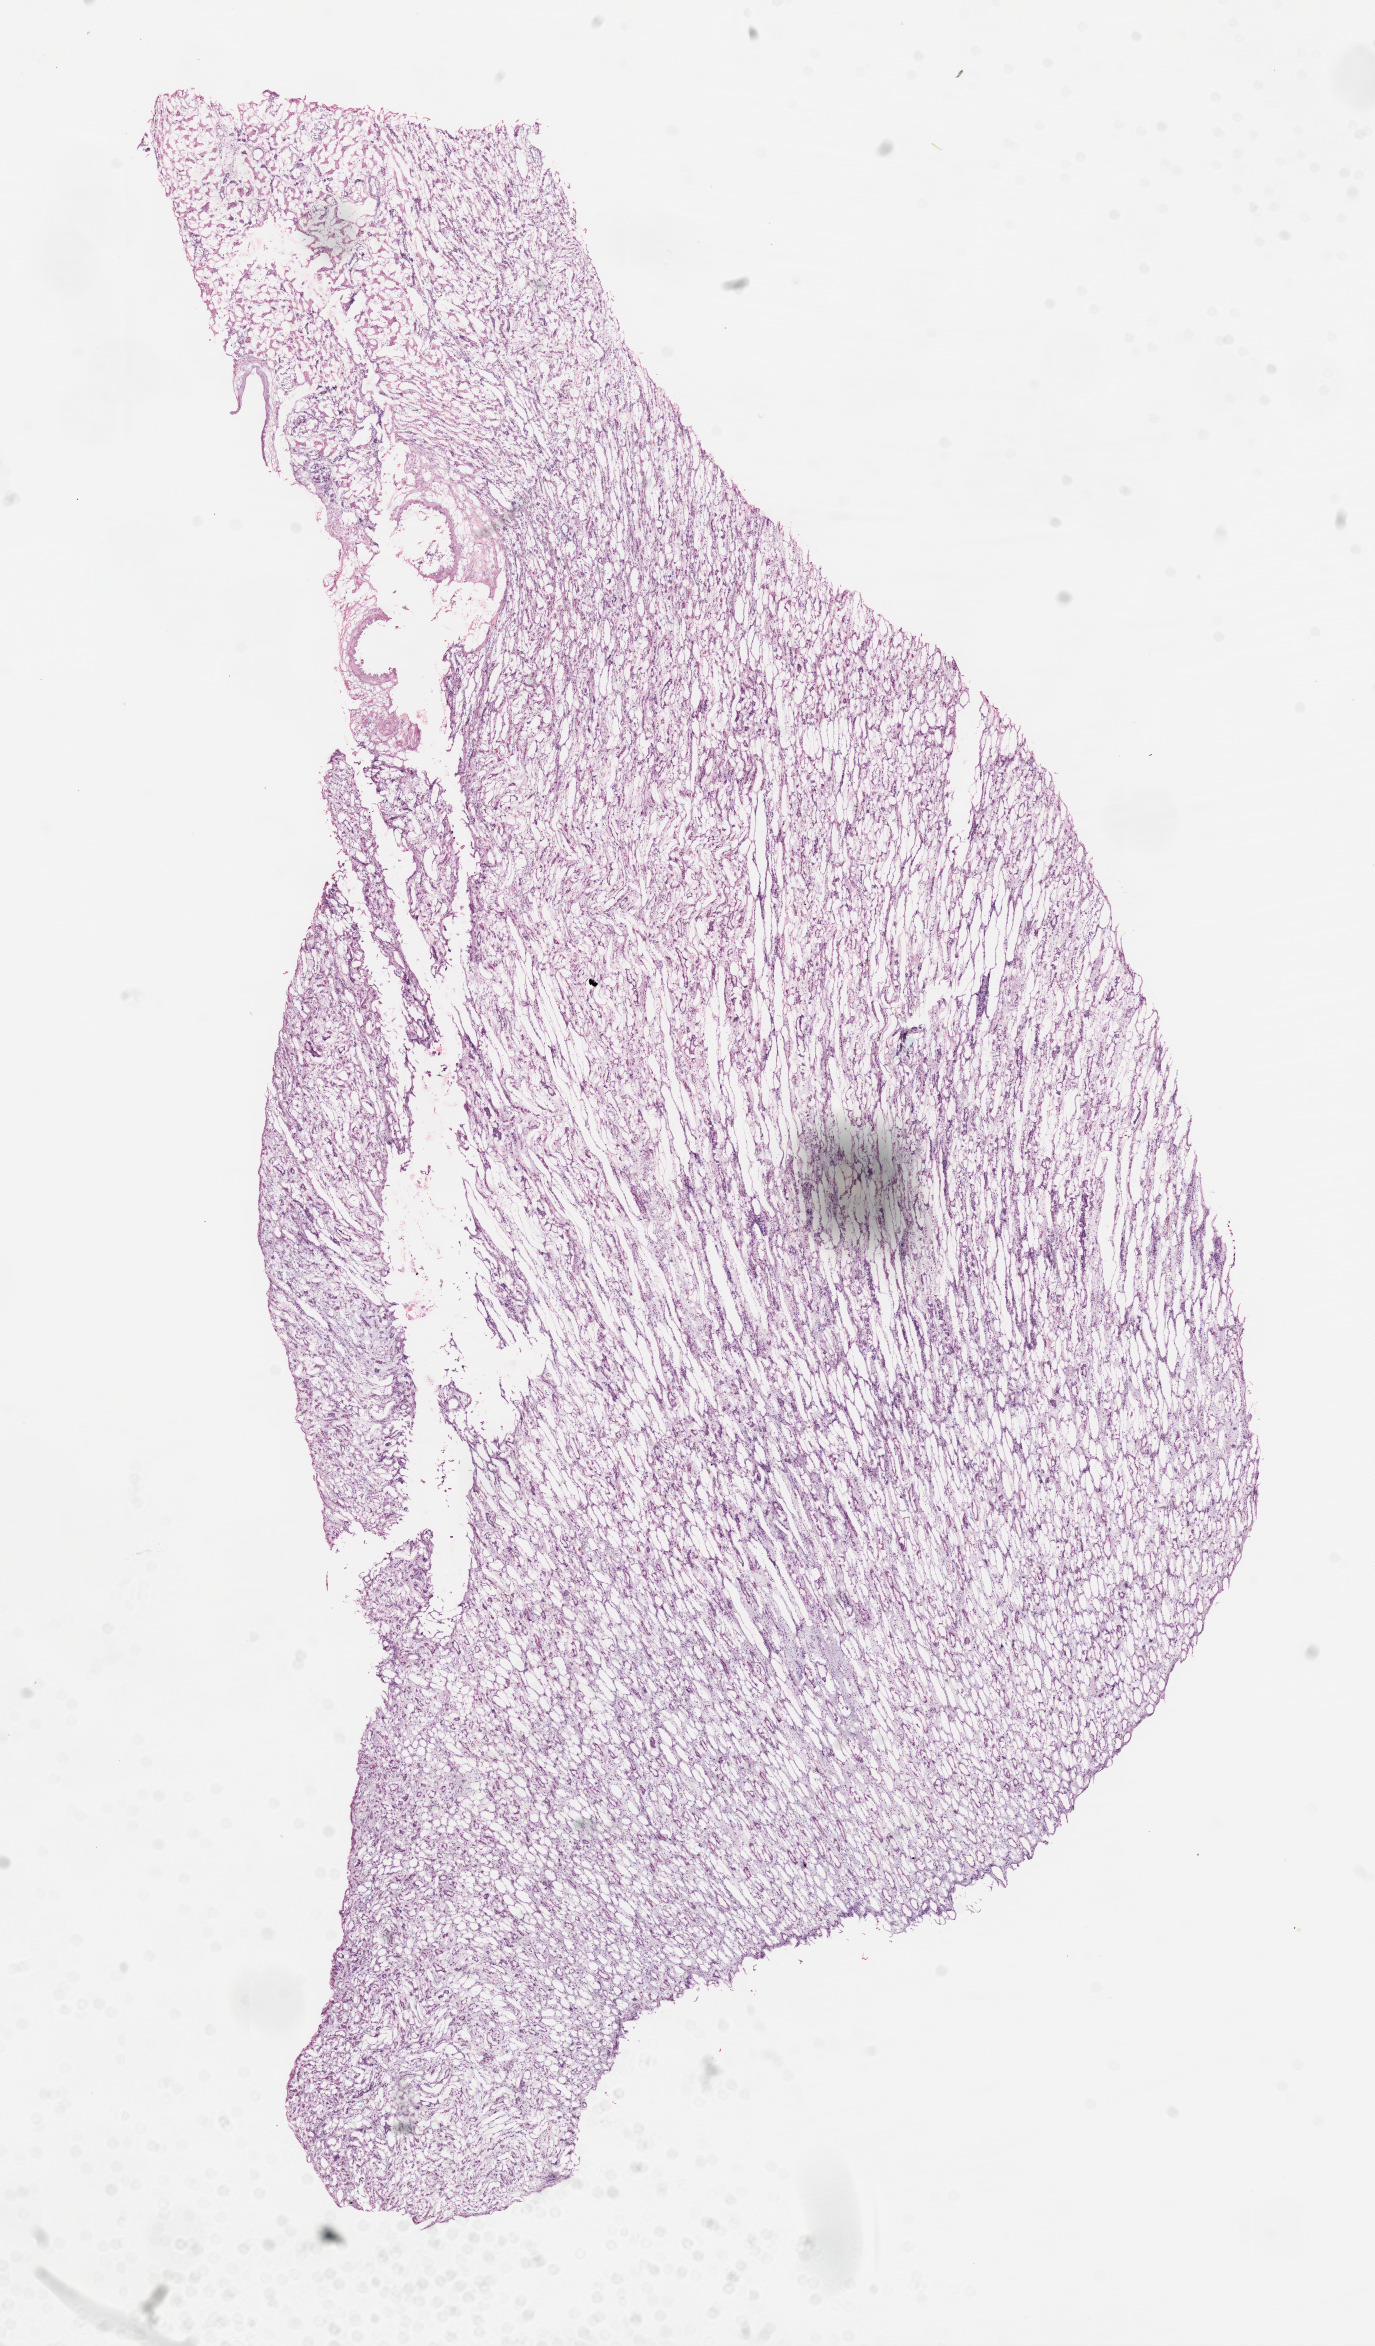
Whole-slide histology image, H&E, whole scanned area (about 11.0 x 18.8 mm, slide scanned at 20x) shown as a low-resolution overview; frozen section from the top of the tissue portion; sample: solid tissue normal (non-tumour tissue), kidney. Male, age 39 years at initial diagnosis.
* this section: solid tissue normal sample (biorepository sample class)
* patient diagnosis: Clear cell adenocarcinoma, NOS